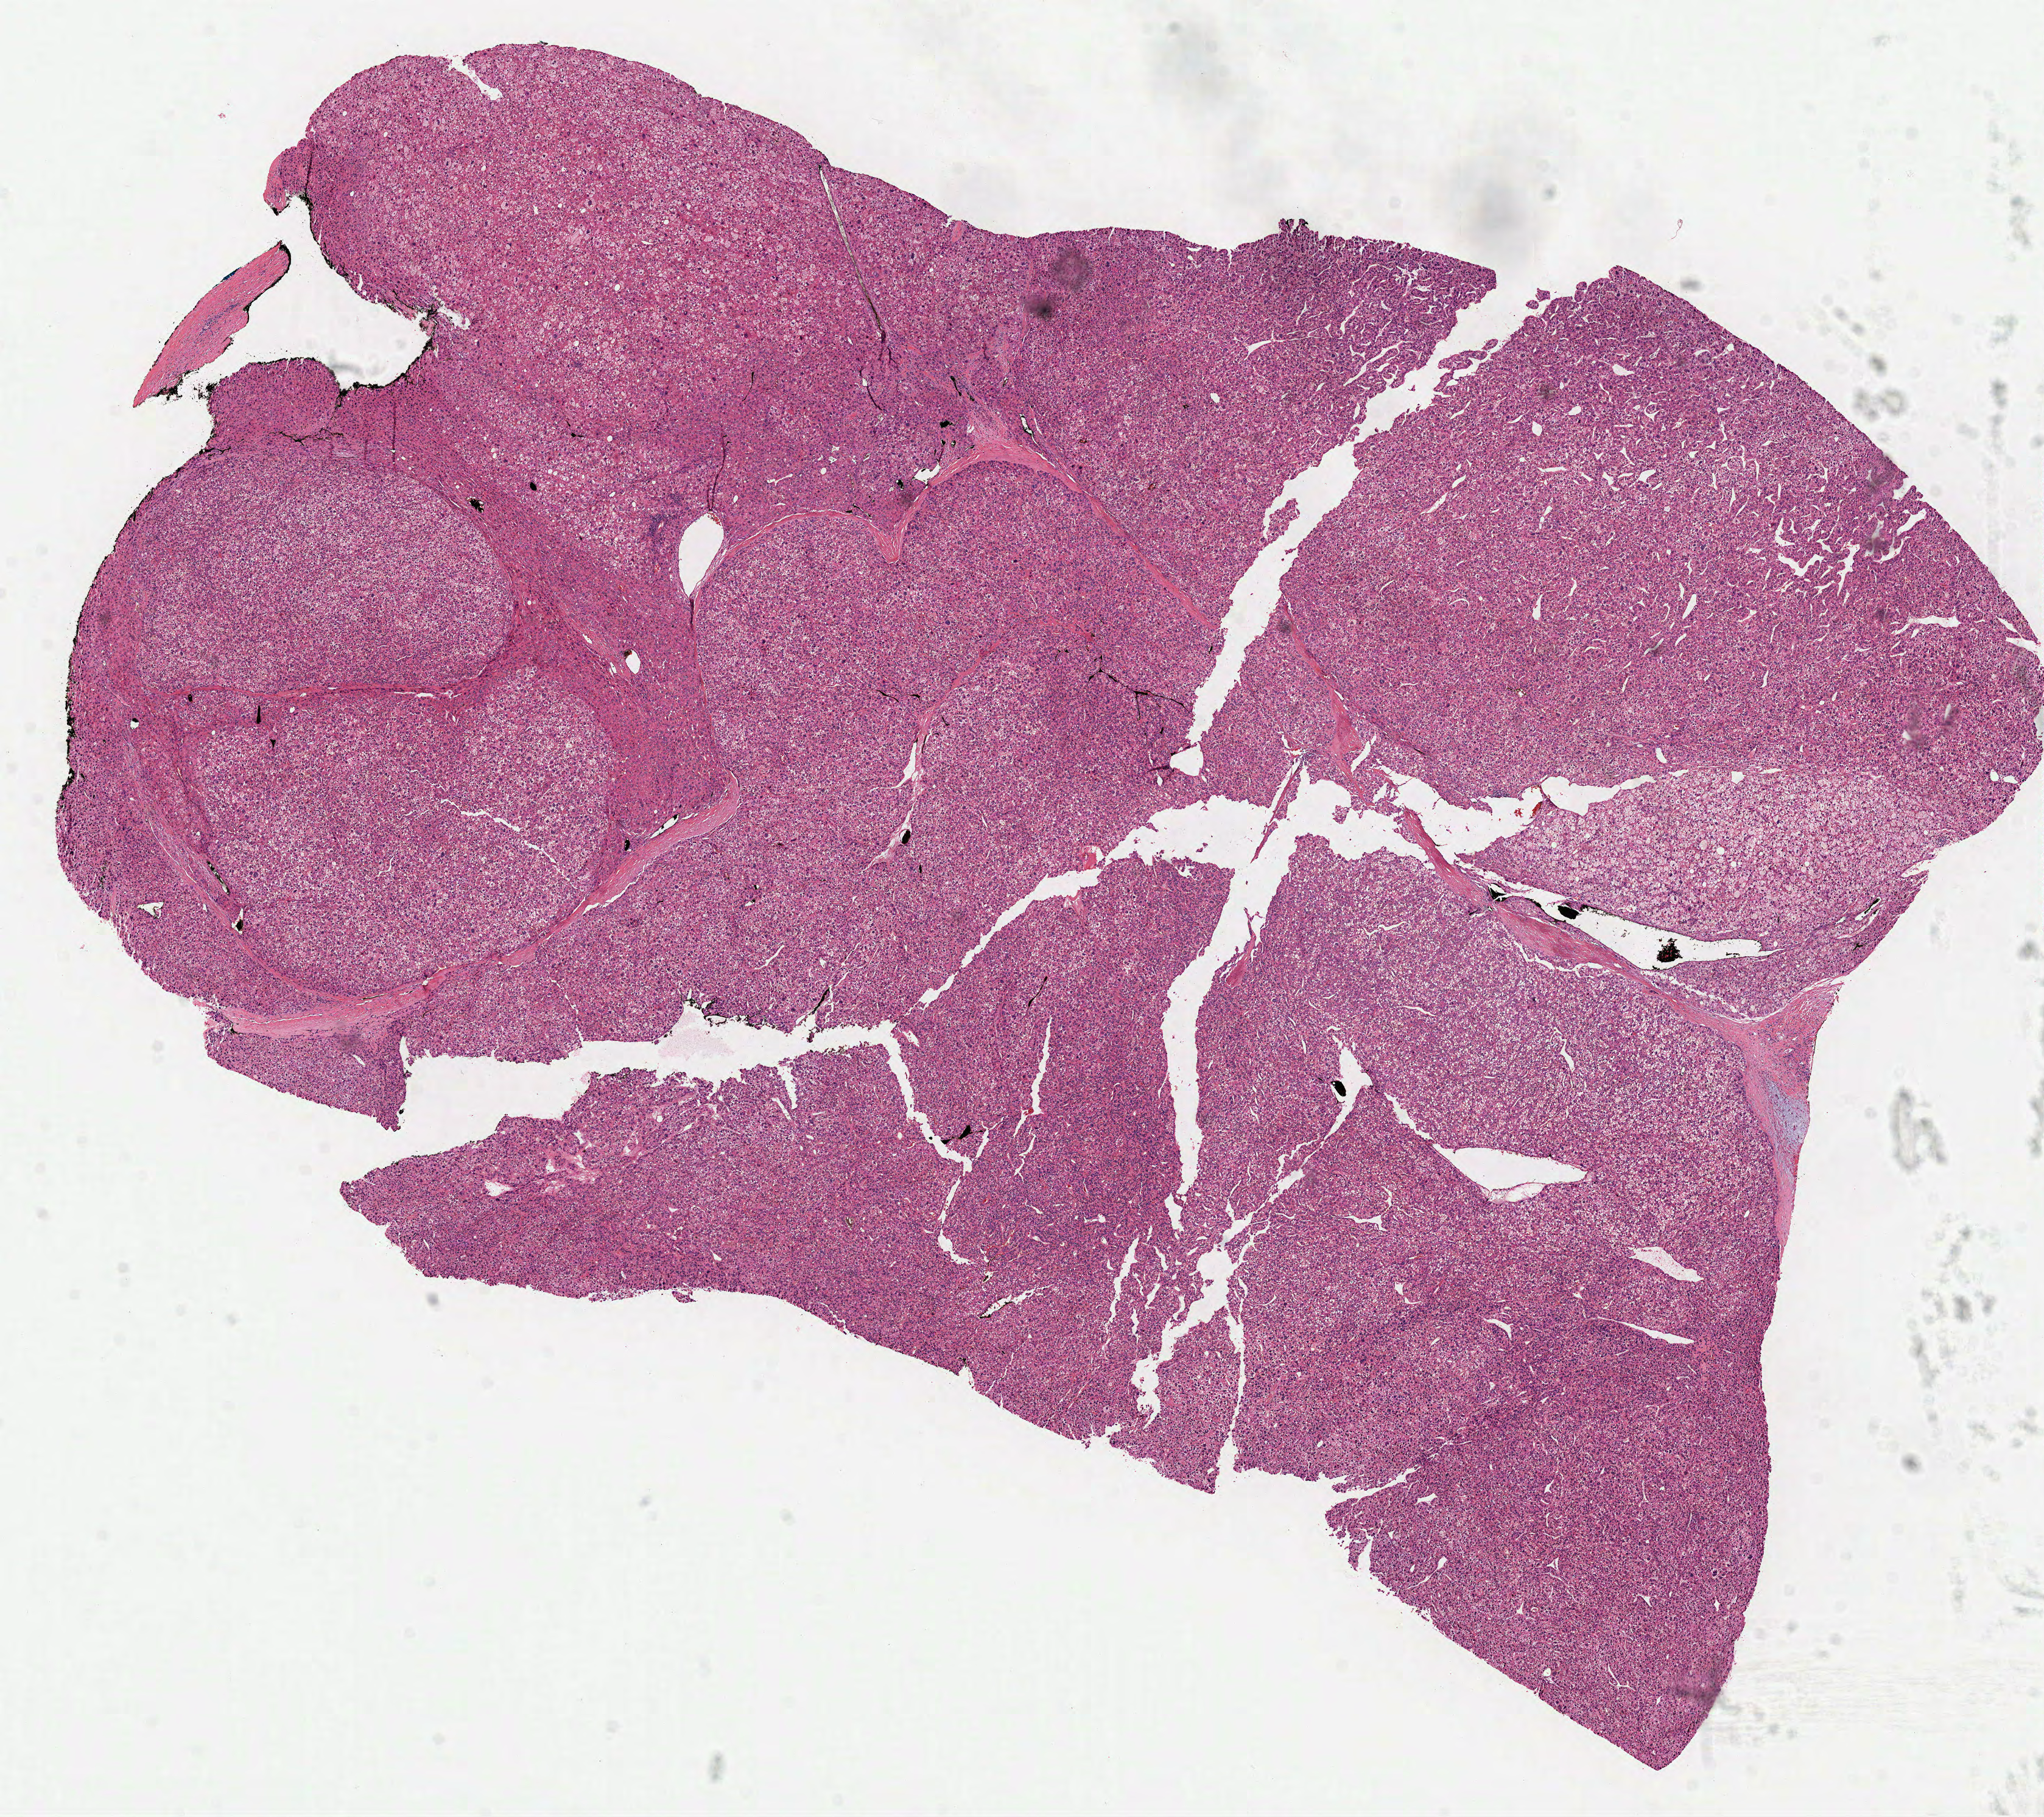
Hematoxylin and eosin (H&E) stained whole-slide image, low-resolution overview of the scanned area, about 13.5 x 12.0 mm (acquisition: 40x scan). FFPE section. Sample: primary tumour, liver. Female patient; age at initial diagnosis 84 years. Histologic grade: G2 (moderately differentiated).
- AJCC pathologic stage: I (7th edition)
- TNM: T1 NX M0
- pathologic diagnosis: Hepatocellular carcinoma, NOS